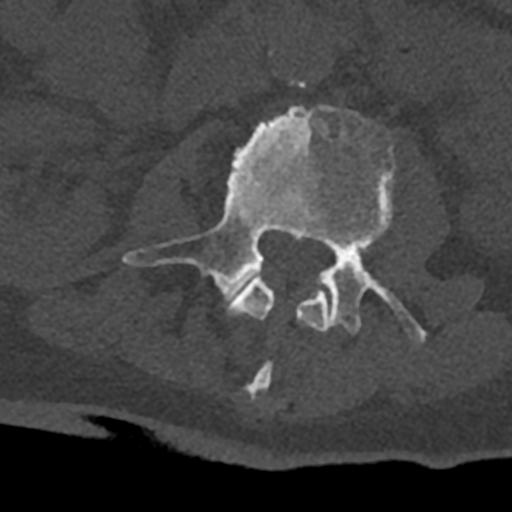
CT including the spine, one axial slice; slice 337 of 797 in the series (ordered by position); reconstruction kernel Br40s/3; 120 kVp; bone window (W 1800 / L 400 HU); 512 × 512 image matrix, field of view 160 × 160 mm. Patient: male, 74 years. From the clinical record (not read from this slice): primary cancer: renal; vertebrae with lytic lesions (as recorded): T10, L1, L2, L3, L4, L5.
Annotated regions visible in this slice (semi-automatic segmentation, software-assisted and operator-edited):
- L2 vertebra: box from (x=227, y=273) to (x=330, y=400) px
- L3 vertebra: (x=122, y=104)–(x=426, y=342)